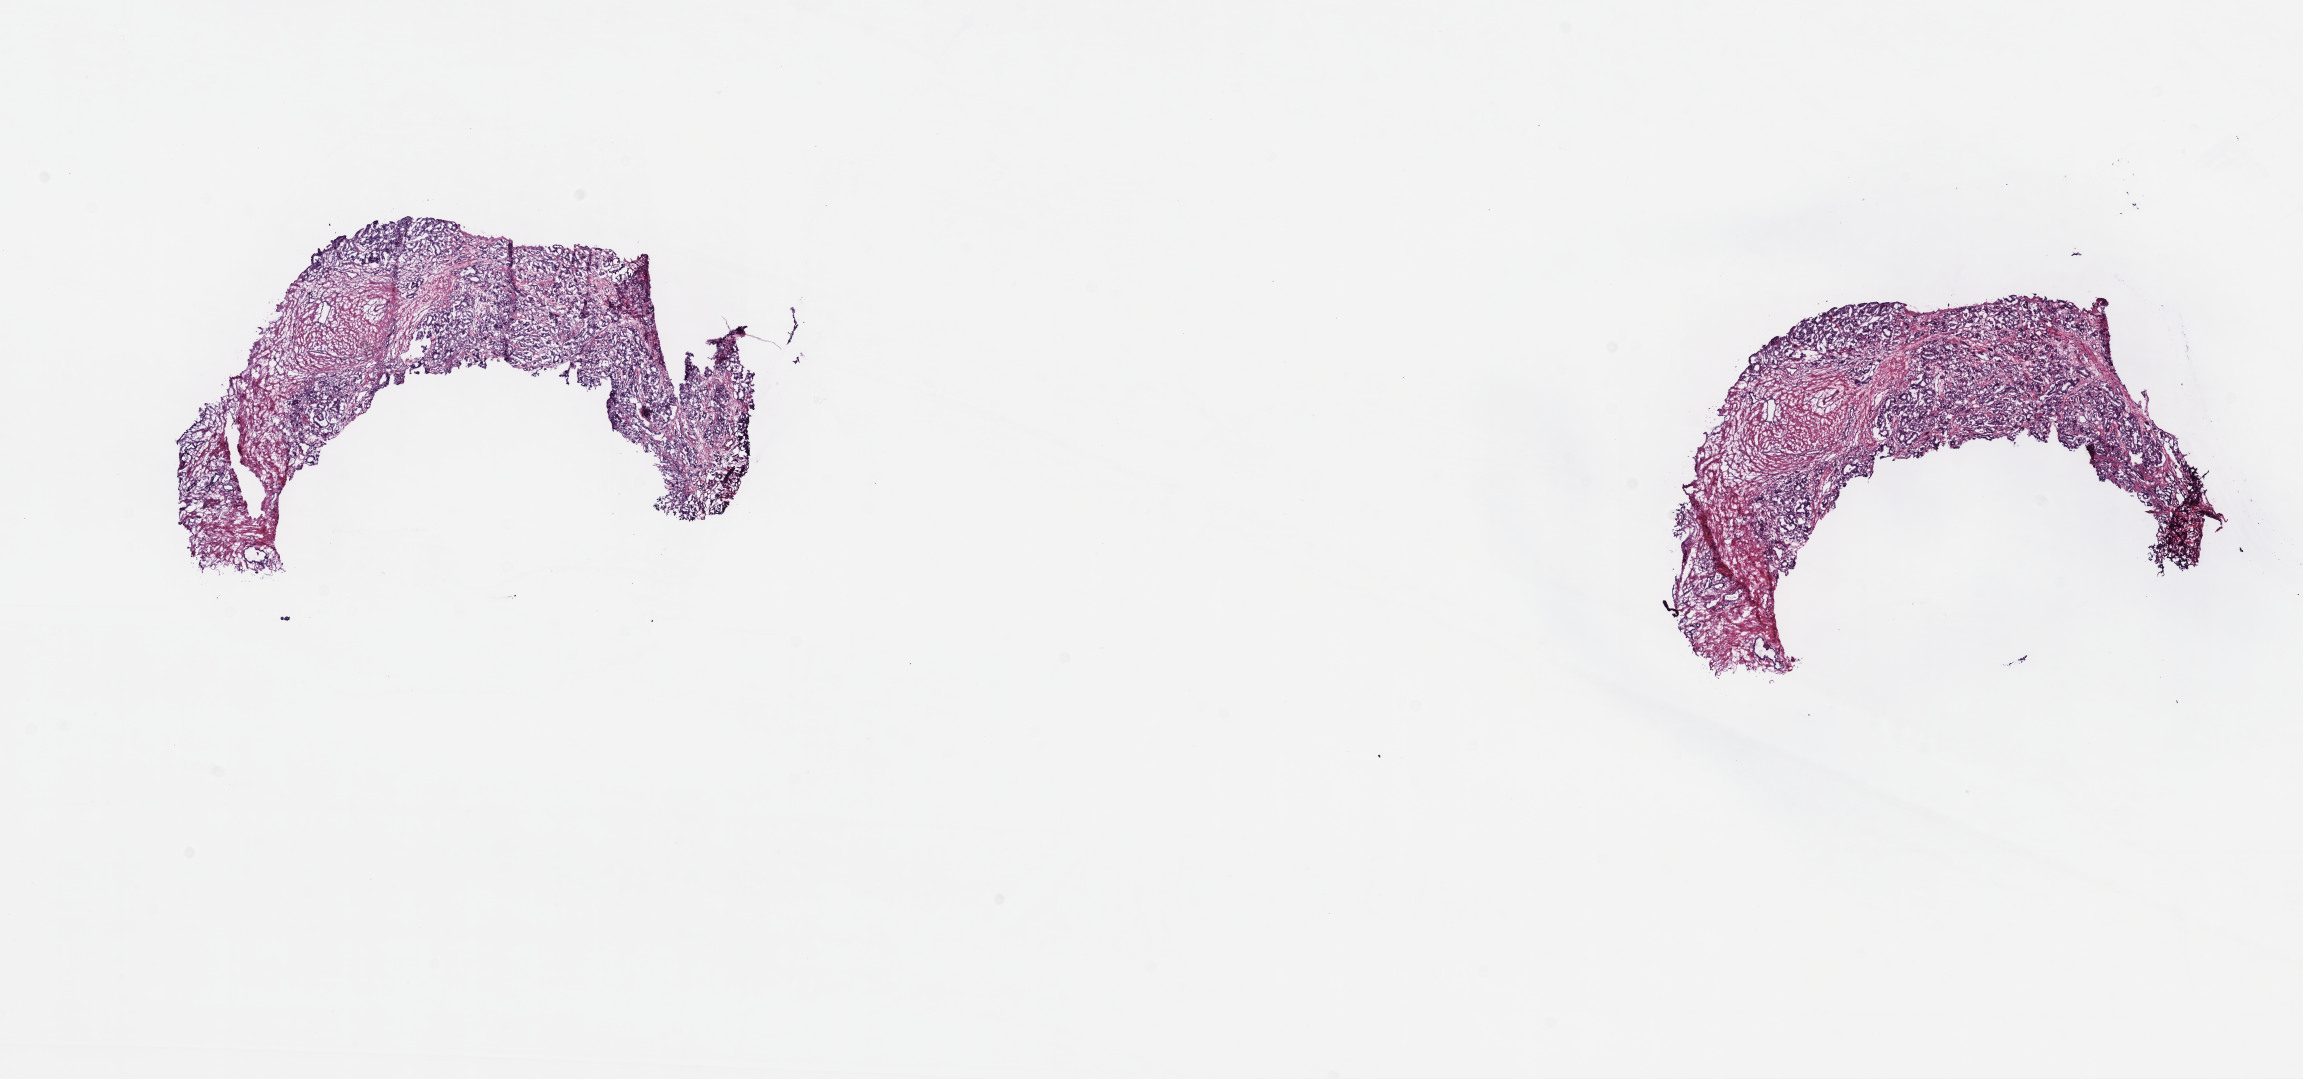
Digitized Hematoxylin and eosin (H&E) stained tissue section (whole slide) — whole scanned area (about 18.6 x 8.7 mm) shown as a low-resolution overview. Frozen section from the top of the tissue portion. Primary tumour sample from the prostate. Patient: male, age at initial diagnosis 66 years. Gleason score: 7 (4+3). Slide review estimates, as recorded: tumour cells 60%, tumour nuclei 70%, normal cells 2%, stromal cells 38%, necrosis 0%. Inflammatory infiltration, as recorded: lymphocyte infiltration 0%, monocyte infiltration 0%, neutrophil infiltration 0%.
Pathologic diagnosis: Adenocarcinoma, NOS (prostate gland).